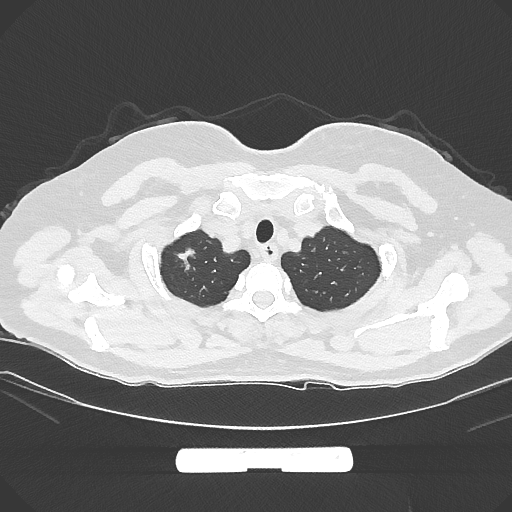
Chest CT, one axial slice. Position 264 of 294 along the scan axis. Reconstruction kernel IMR1,SharpPlus. 120 kVp. Lung window (W 1500 / L -600 HU). 1 mm slice thickness. 512 × 512 image matrix, field of view 369 × 369 mm. Patient: female, 58 years. From the clinical record (not read from this slice): clinical TNM (as recorded): T1b N0 M0; histopathological grade: G2-3.
Outlined on this slice (rectangle marked by the reading radiologist):
- lung tumour (recorded histology: adenocarcinoma): box from (x=169, y=243) to (x=201, y=271) px